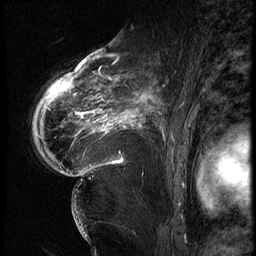
Breast MRI (dynamic contrast-enhanced), one sagittal slice. Slice 44 of 62 in the series (ordered by position). 3 images stored at this slice position (order not interpretable as contrast timing). 1.5 T. TE 4.2 ms, TR 9 ms. 2.5 mm slice thickness. 256 × 256 image matrix, field of view 180 × 180 mm. Female patient, age 56 years. From the clinical record (not read from this slice): setting: breast cancer imaged before/during neoadjuvant chemotherapy; receptor status: HER2-positive.
Annotated regions visible in this slice (semi-automatic segmentation, software-assisted and operator-edited):
- analysis volume of interest (the breast-tissue region the enhancement analysis was run in; not a lesion): bounding box (x1, y1, x2, y2) in pixels: (84, 75, 181, 153)
- tumour enhancement mask (voxels above the 140 % enhancement threshold inside the analysis volume of interest): (92, 81, 162, 133)